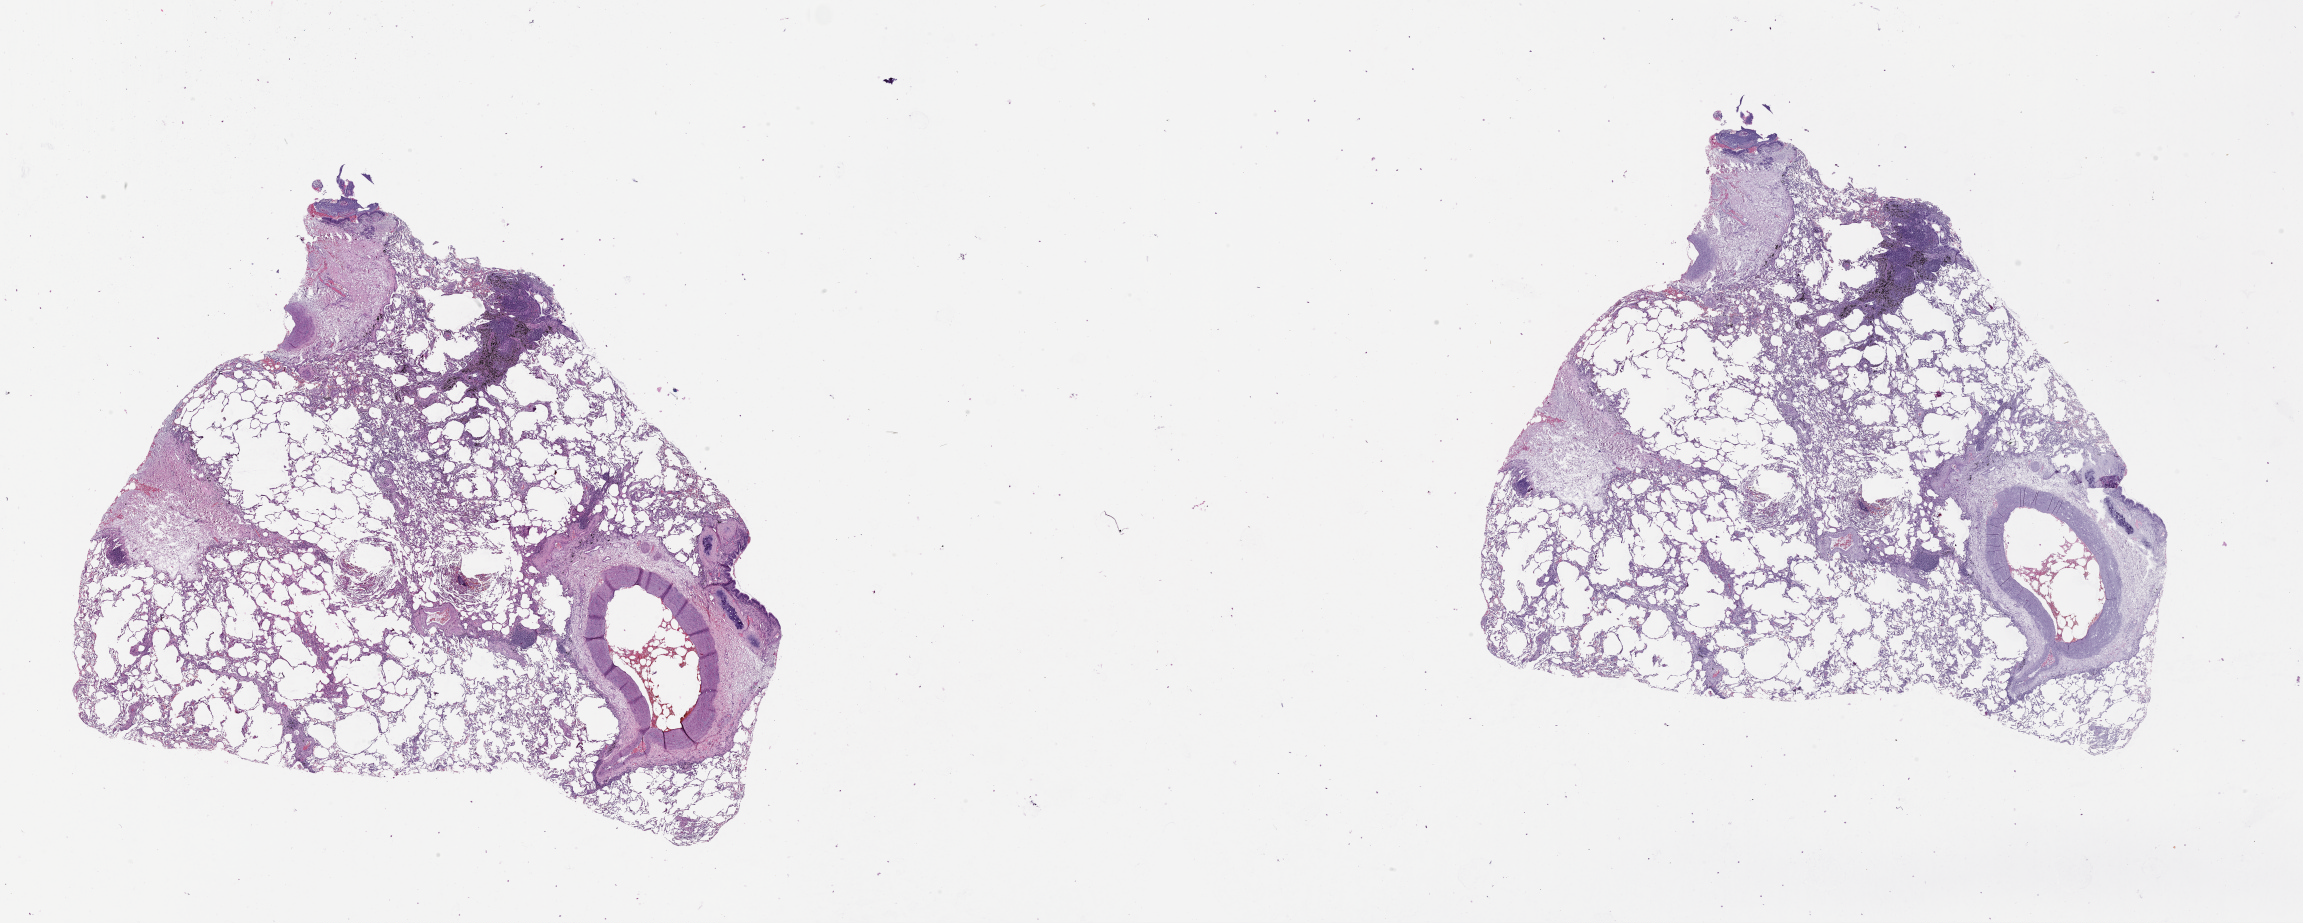
H&E-stained whole-slide image, shown as a low-resolution overview of the whole scanned area (about 37.1 x 14.9 mm); lung, tissue type not recorded.
Patient diagnosis (cohort enrolment): squamous cell carcinoma (lung).